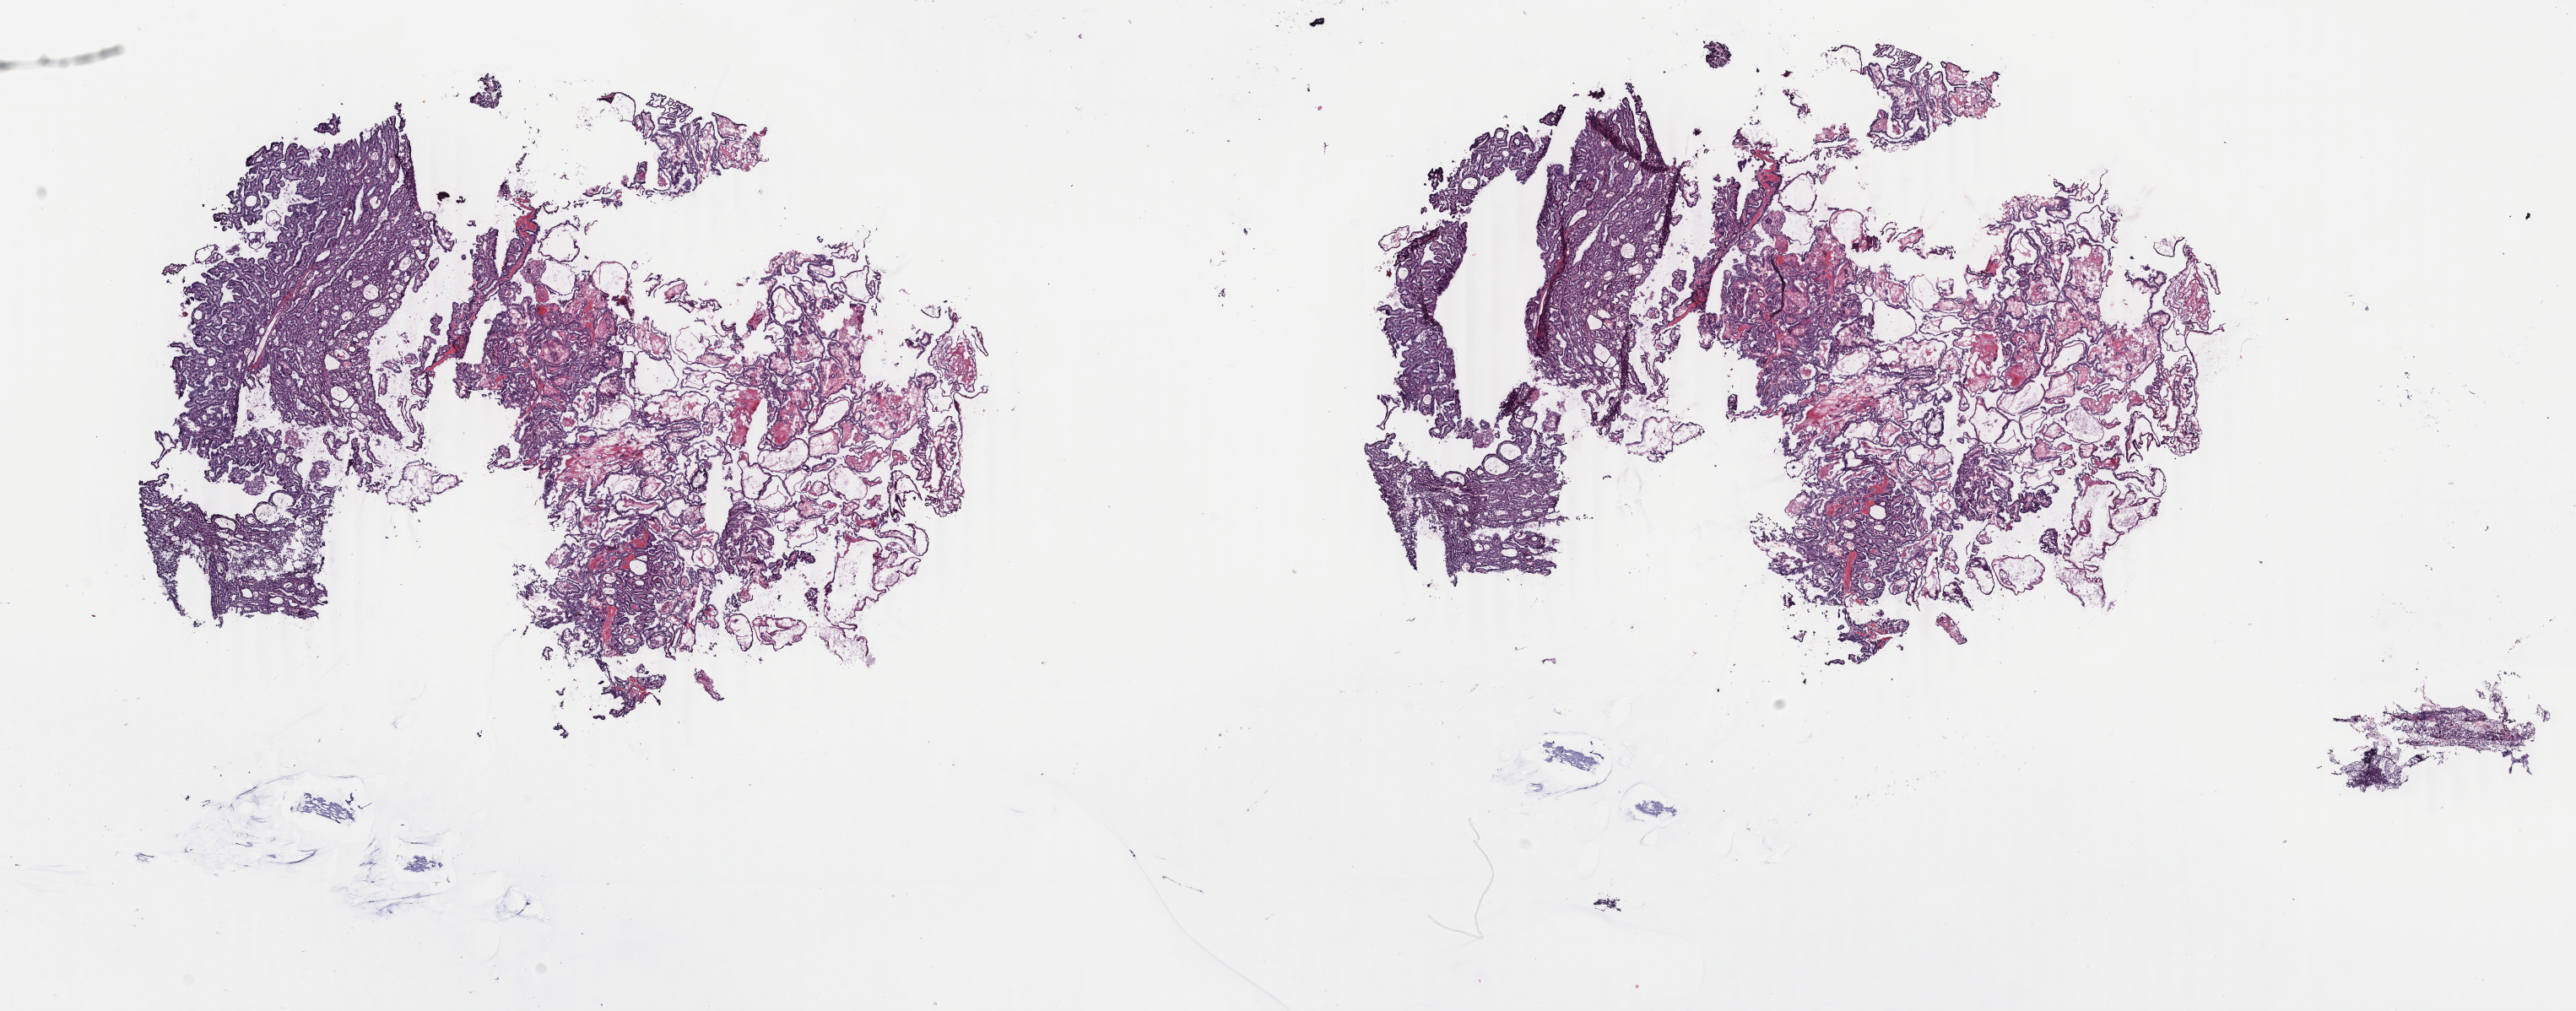
H&E-stained whole-slide image, shown as a low-resolution overview of the whole scanned area (about 24.3 x 9.5 mm), frozen section from the top of the tissue portion, thyroid, primary tumour sample. Patient: female, age at initial diagnosis 41 years. Composition of this section per pathologist review: tumour cells 90%, tumour nuclei 95%, normal cells 0%, stromal cells 10%, necrosis 0%. Inflammatory infiltration, as recorded: lymphocyte infiltration 0%, monocyte infiltration 0%, neutrophil infiltration 0%.
AJCC pathologic stage: I (7th edition). Diagnosis: Papillary adenocarcinoma, NOS (thyroid gland).